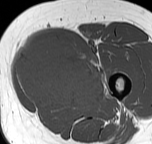
MRI of an extremity soft-tissue mass, one axial slice. Position 23 of 57 along the scan axis. MR volume resampled by the dataset authors to the PET/CT grid (not the native acquisition matrix). 152 × 144 image matrix. Female patient. From the clinical record (not read from this slice): histological type: pleiomorphic leiomyosarcoma; grade: intermediate; site of the primary tumour: left thigh.
Structures marked on this image (expert contour drawn on MRI and transferred to this co-registered scan by the dataset authors):
- gross tumour volume including surrounding oedema: bounding box <15,40,110,113> (left, top, right, bottom; pixels)
- gross tumour volume (mass): <15,40,105,111>